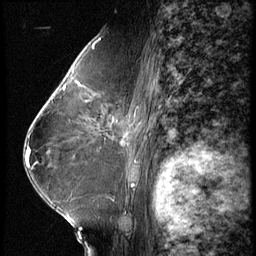
Breast MRI (dynamic contrast-enhanced), one sagittal slice; position 37 of 62 along the scan axis; 3 images stored at this slice position (order not interpretable as contrast timing); 1.5 T; TE 4.2 ms, TR 9 ms; 2.5 mm slice thickness; 256 × 256 image matrix, field of view 180 × 180 mm. Patient: female, 65 years. Case-level facts recorded for this patient, not image findings: setting: breast cancer imaged before/during neoadjuvant chemotherapy; receptor status: HR-positive, HER2-negative.
Structures marked on this image (semi-automatically segmented with operator editing):
- analysis volume of interest (the breast-tissue region the enhancement analysis was run in; not a lesion): bounding box [x1, y1, x2, y2] px = [104, 104, 154, 161]
- tumour enhancement mask (voxels above the 140 % enhancement threshold inside the analysis volume of interest): [121, 139, 126, 146]